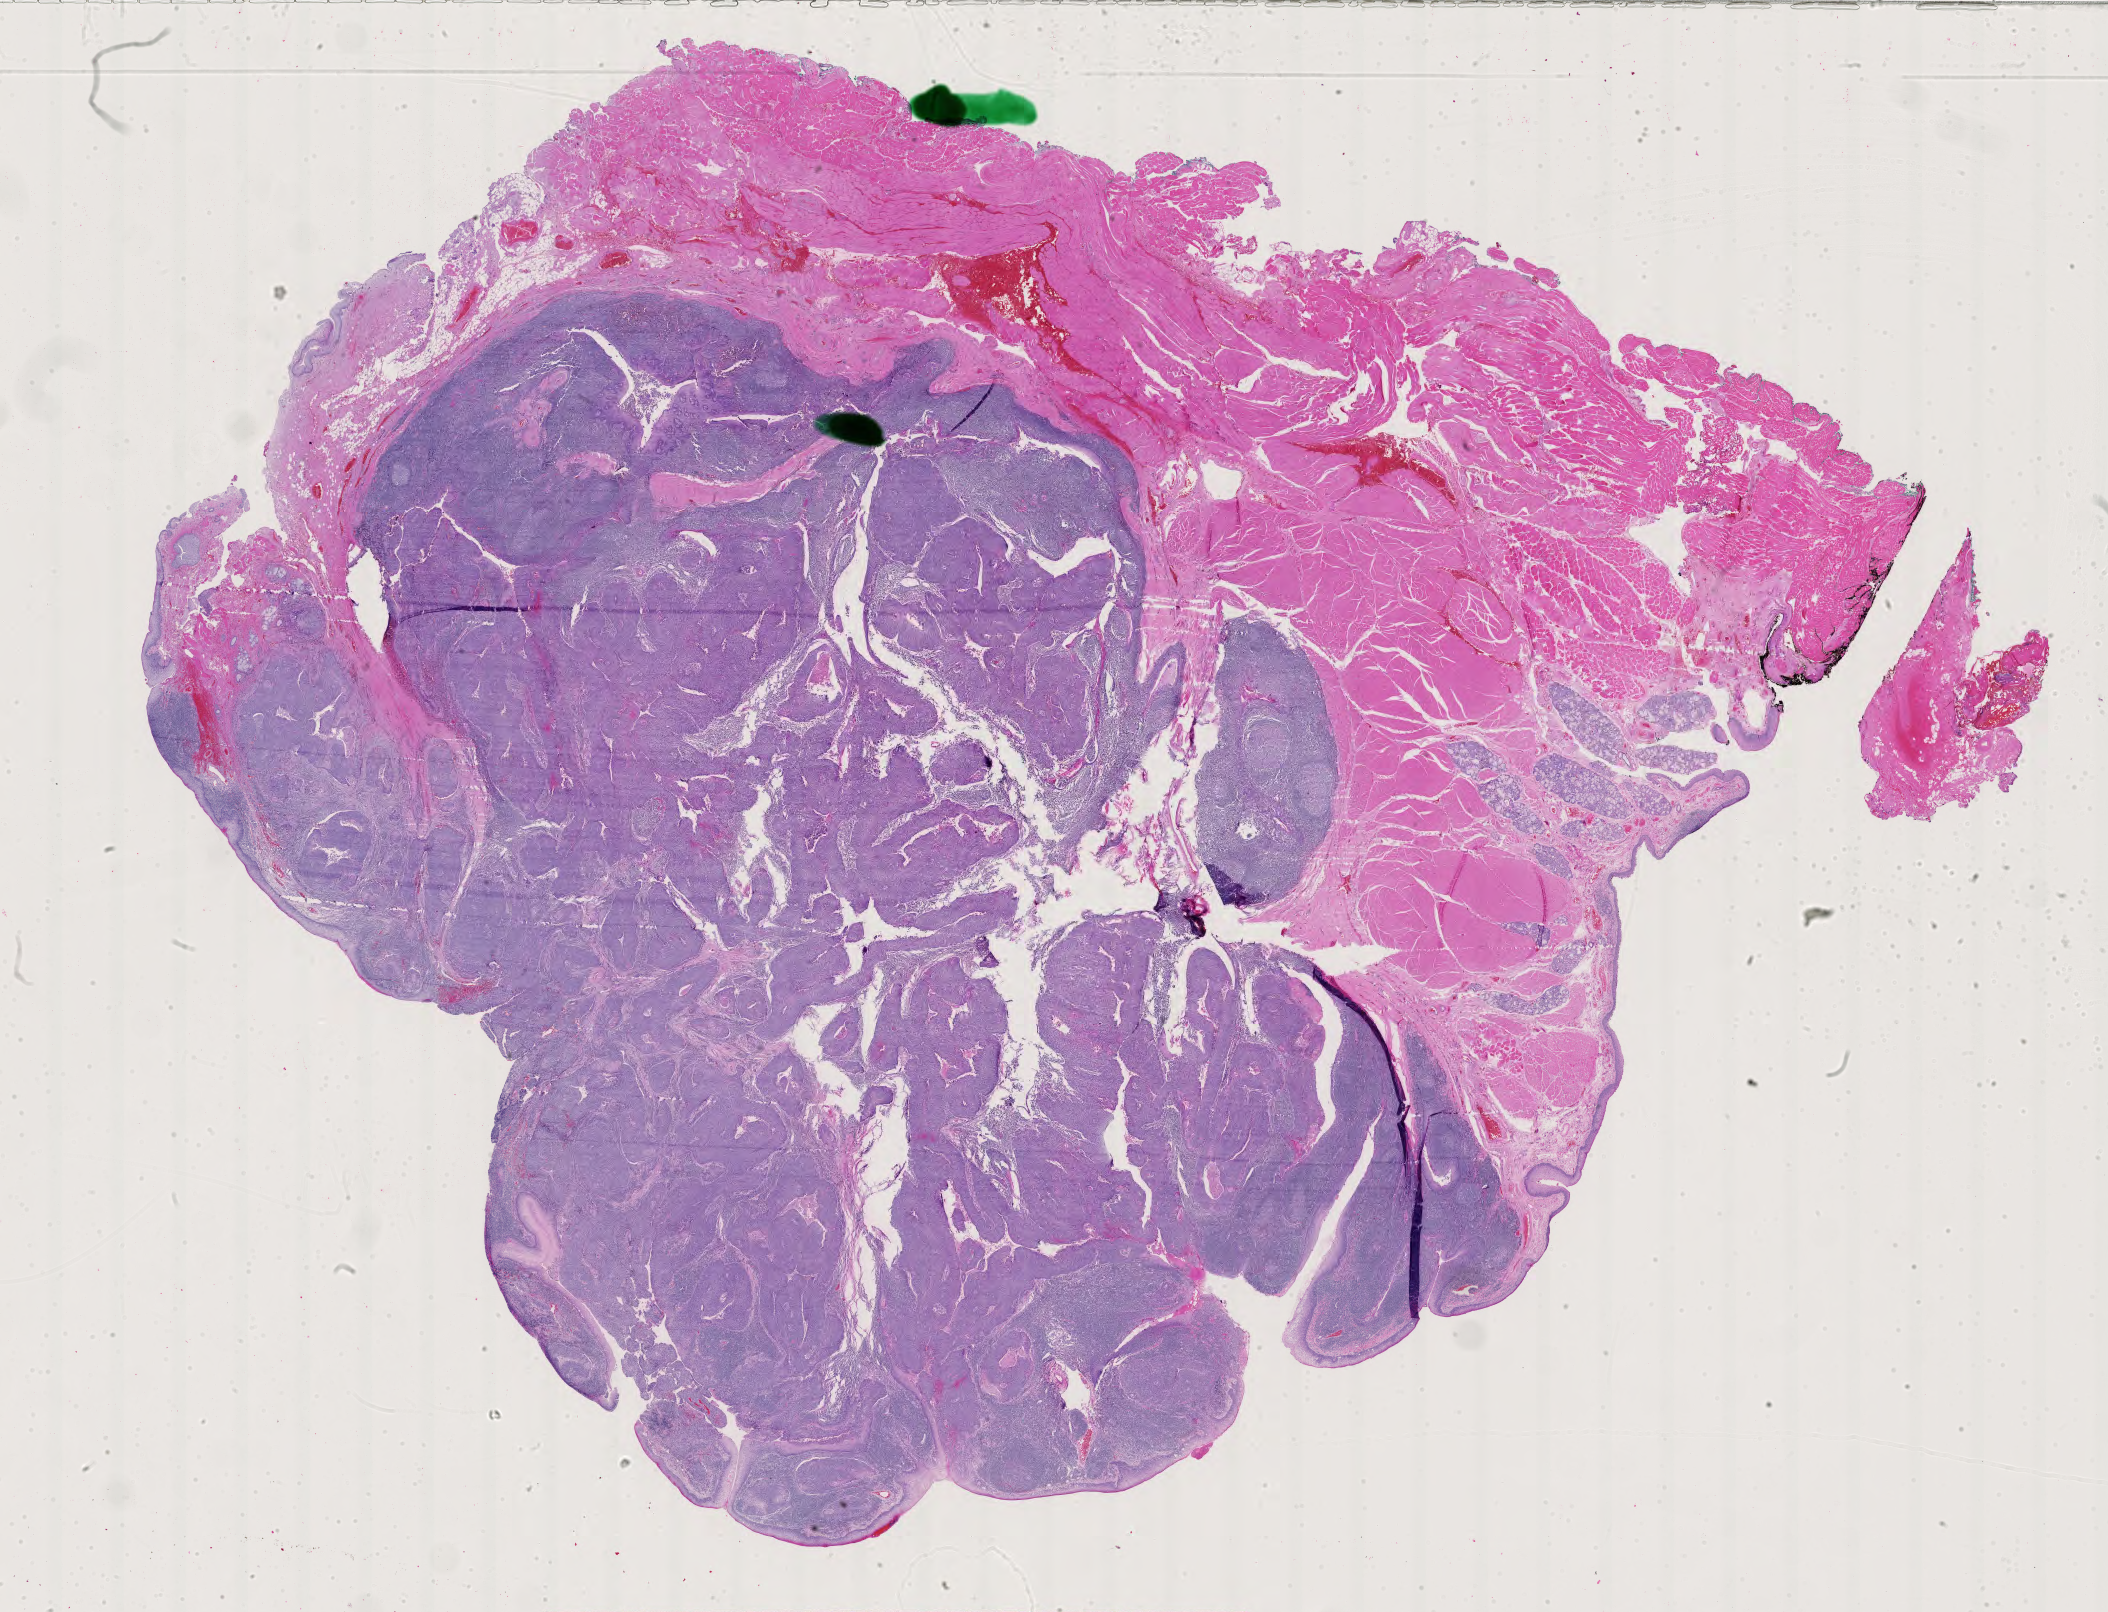
Digitized H&E-stained tissue section (whole slide) — shown as a low-resolution overview of the whole scanned area (about 30.6 x 23.4 mm, acquisition: 40x scan), formalin-fixed paraffin-embedded (FFPE) diagnostic section, sample: primary tumour, head and neck. Male, age 56 years at initial diagnosis. Histologic grade: G2 (moderately differentiated).
- pathologic diagnosis: Squamous cell carcinoma, NOS
- AJCC pathologic stage: II